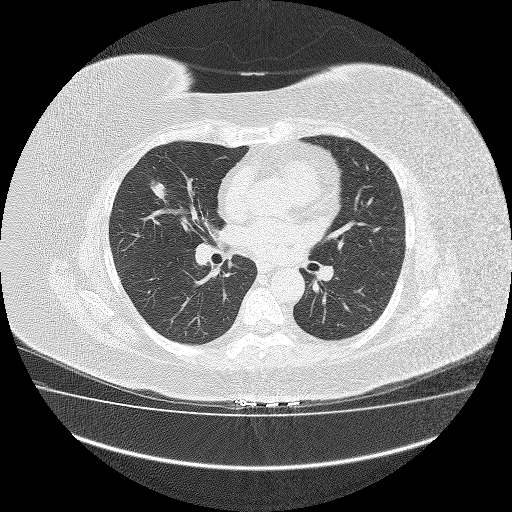
Axial slice from a low-dose chest CT screening exam; third screening round (two years after baseline); lung window (W 1500 / L -600 HU); lung (sharp) reconstruction kernel (FC51); slice 75 of 162 in the series. Female participant, aged 64 years at enrolment.
Expert-annotated lung lesion, bounding box <129,167,178,212> (left, top, right, bottom; pixels). Screening reader's record for this exam (one nodule recorded; not confirmed to be the boxed lesion): non-calcified nodule or mass ≥4 mm, right middle lobe, 23 × 13 mm, smooth margins, soft tissue attenuation, pre-existing on the prior screen: no. Official screen result: positive, other. Lung cancer was diagnosed 31 days after this screen: carcinoid tumor, NOS, right middle lobe, 3 mm at pathology.